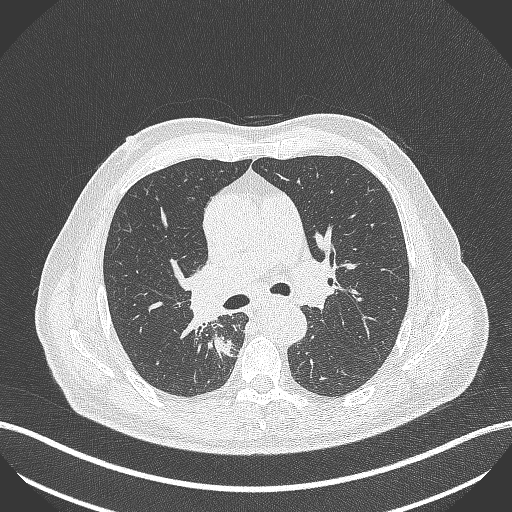
Chest CT, one axial slice. Position 285 of 451 along the scan axis. 100 kVp. Lung window (W 1500 / L -600 HU). 1 mm slice thickness. 512 × 512 image matrix. Male patient, age 61 years. Case-level facts recorded for this patient, not image findings: clinical TNM (as recorded): T1 N0 M0; histopathological grade: G3.
Structures marked on this image (bounding box drawn by a radiologist):
- lung tumour (recorded histology: small cell carcinoma): bounding box [x1, y1, x2, y2] px = [214, 333, 240, 364]